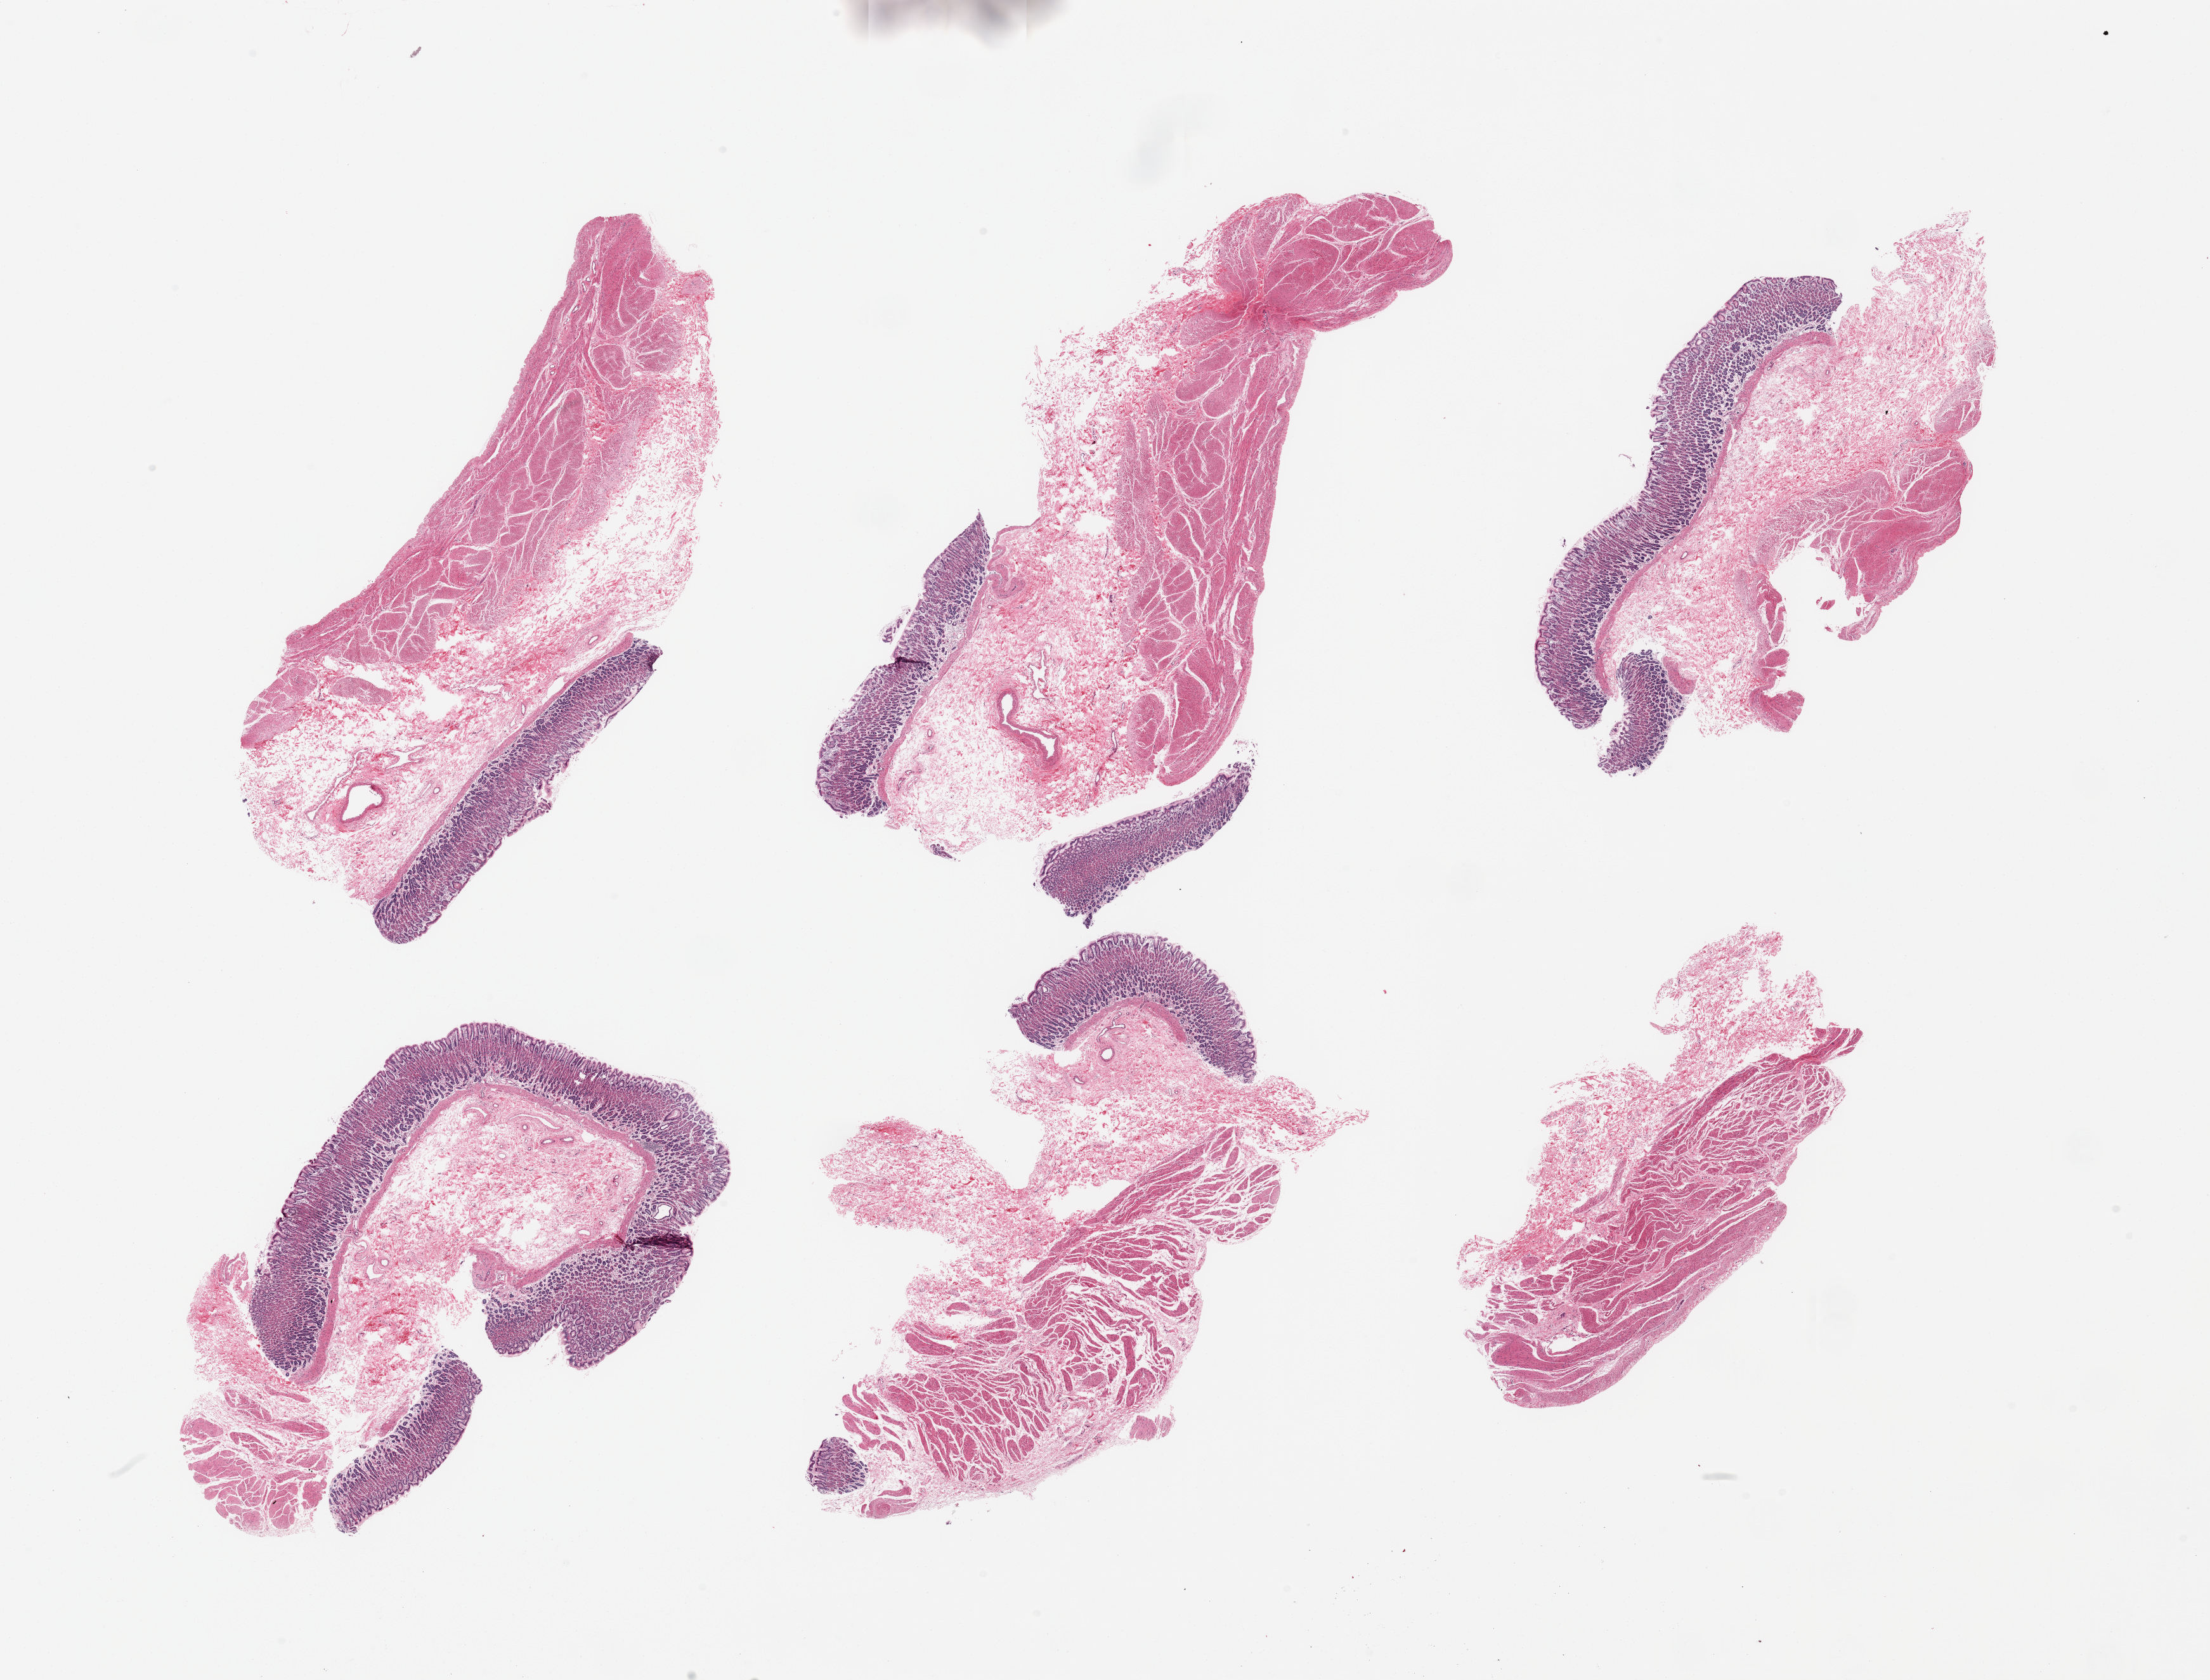
Whole-slide image, haematoxylin and eosin stain, low-resolution overview of the scanned area, about 27.6 x 21.0 mm (from a 20x scan), PAXgene-fixed paraffin-embedded (PFPE) section, section of stomach (target tissue), donor tissue sample. Female donor.
• review note (as recorded): 6 pieces; variable representation of mucosa, submucosa, and muscularis